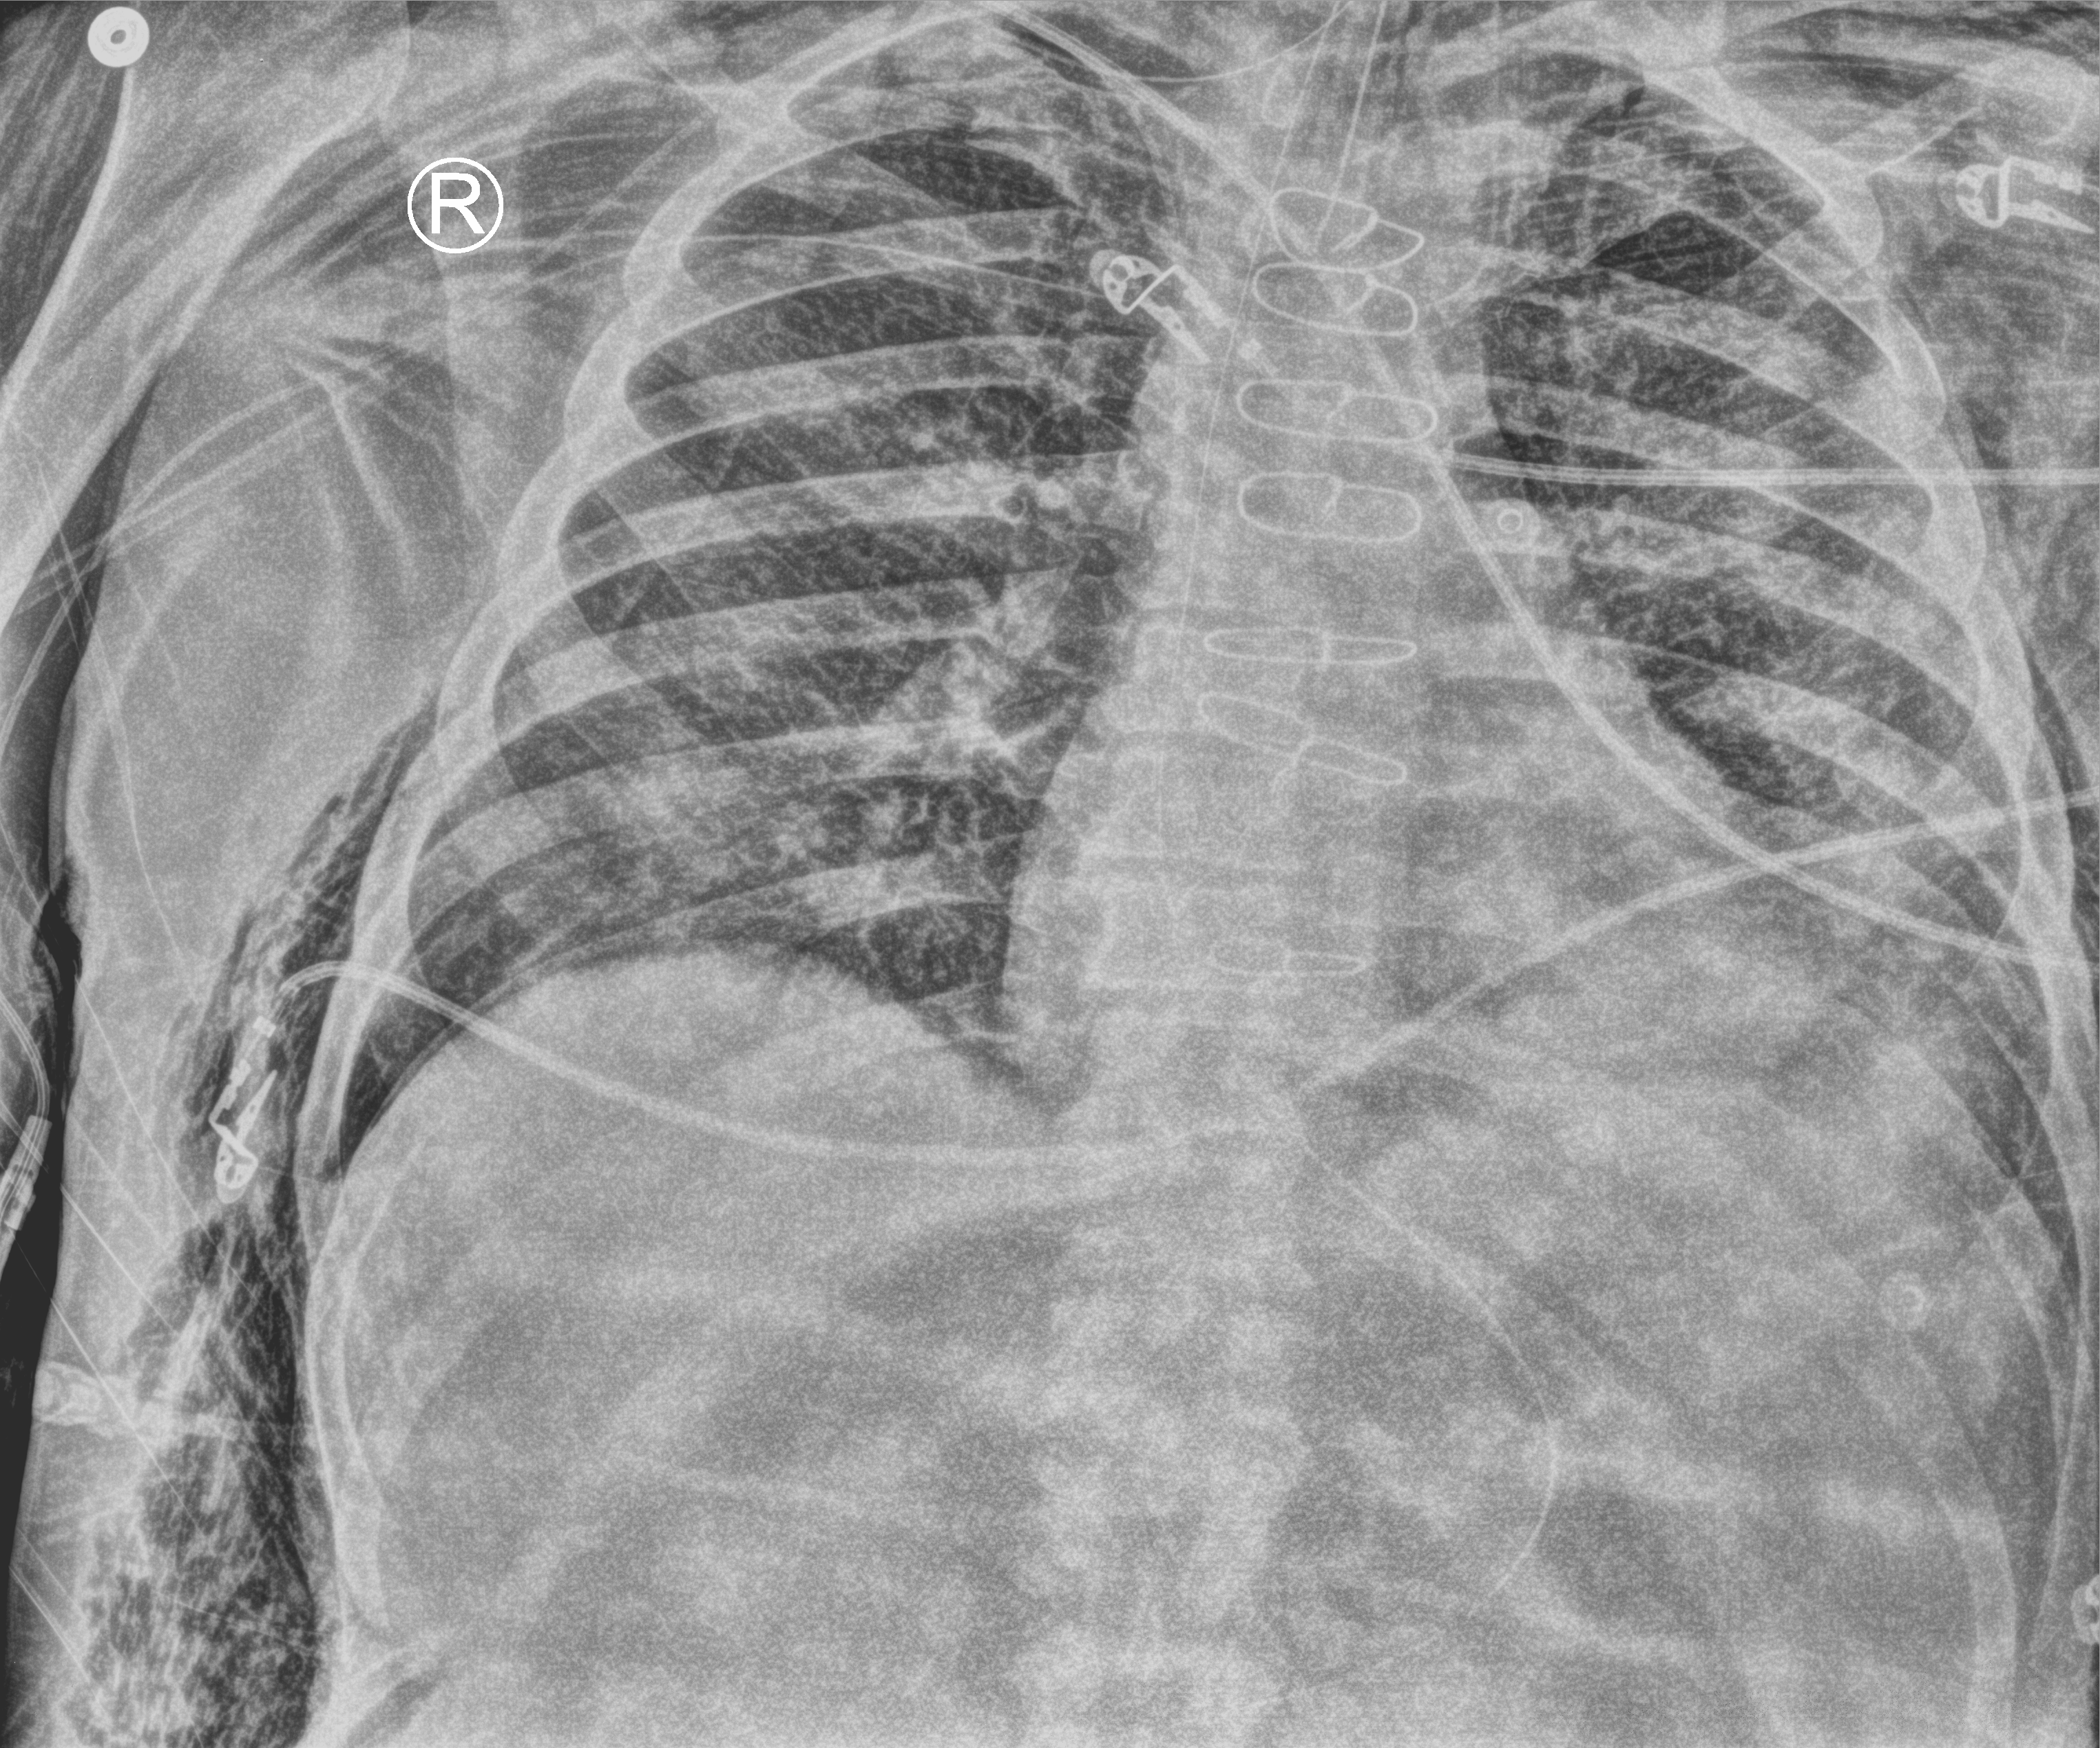
Portable chest radiograph; anteroposterior (AP) projection. Patient hospitalised with COVID-19; male, aged 60–74 years.
Admission-level facts for this patient (not findings on this image; timing relative to this image not recorded): mechanically ventilated during this hospital stay: yes; smoking status (admission record): former; length of hospital stay: 44 days.